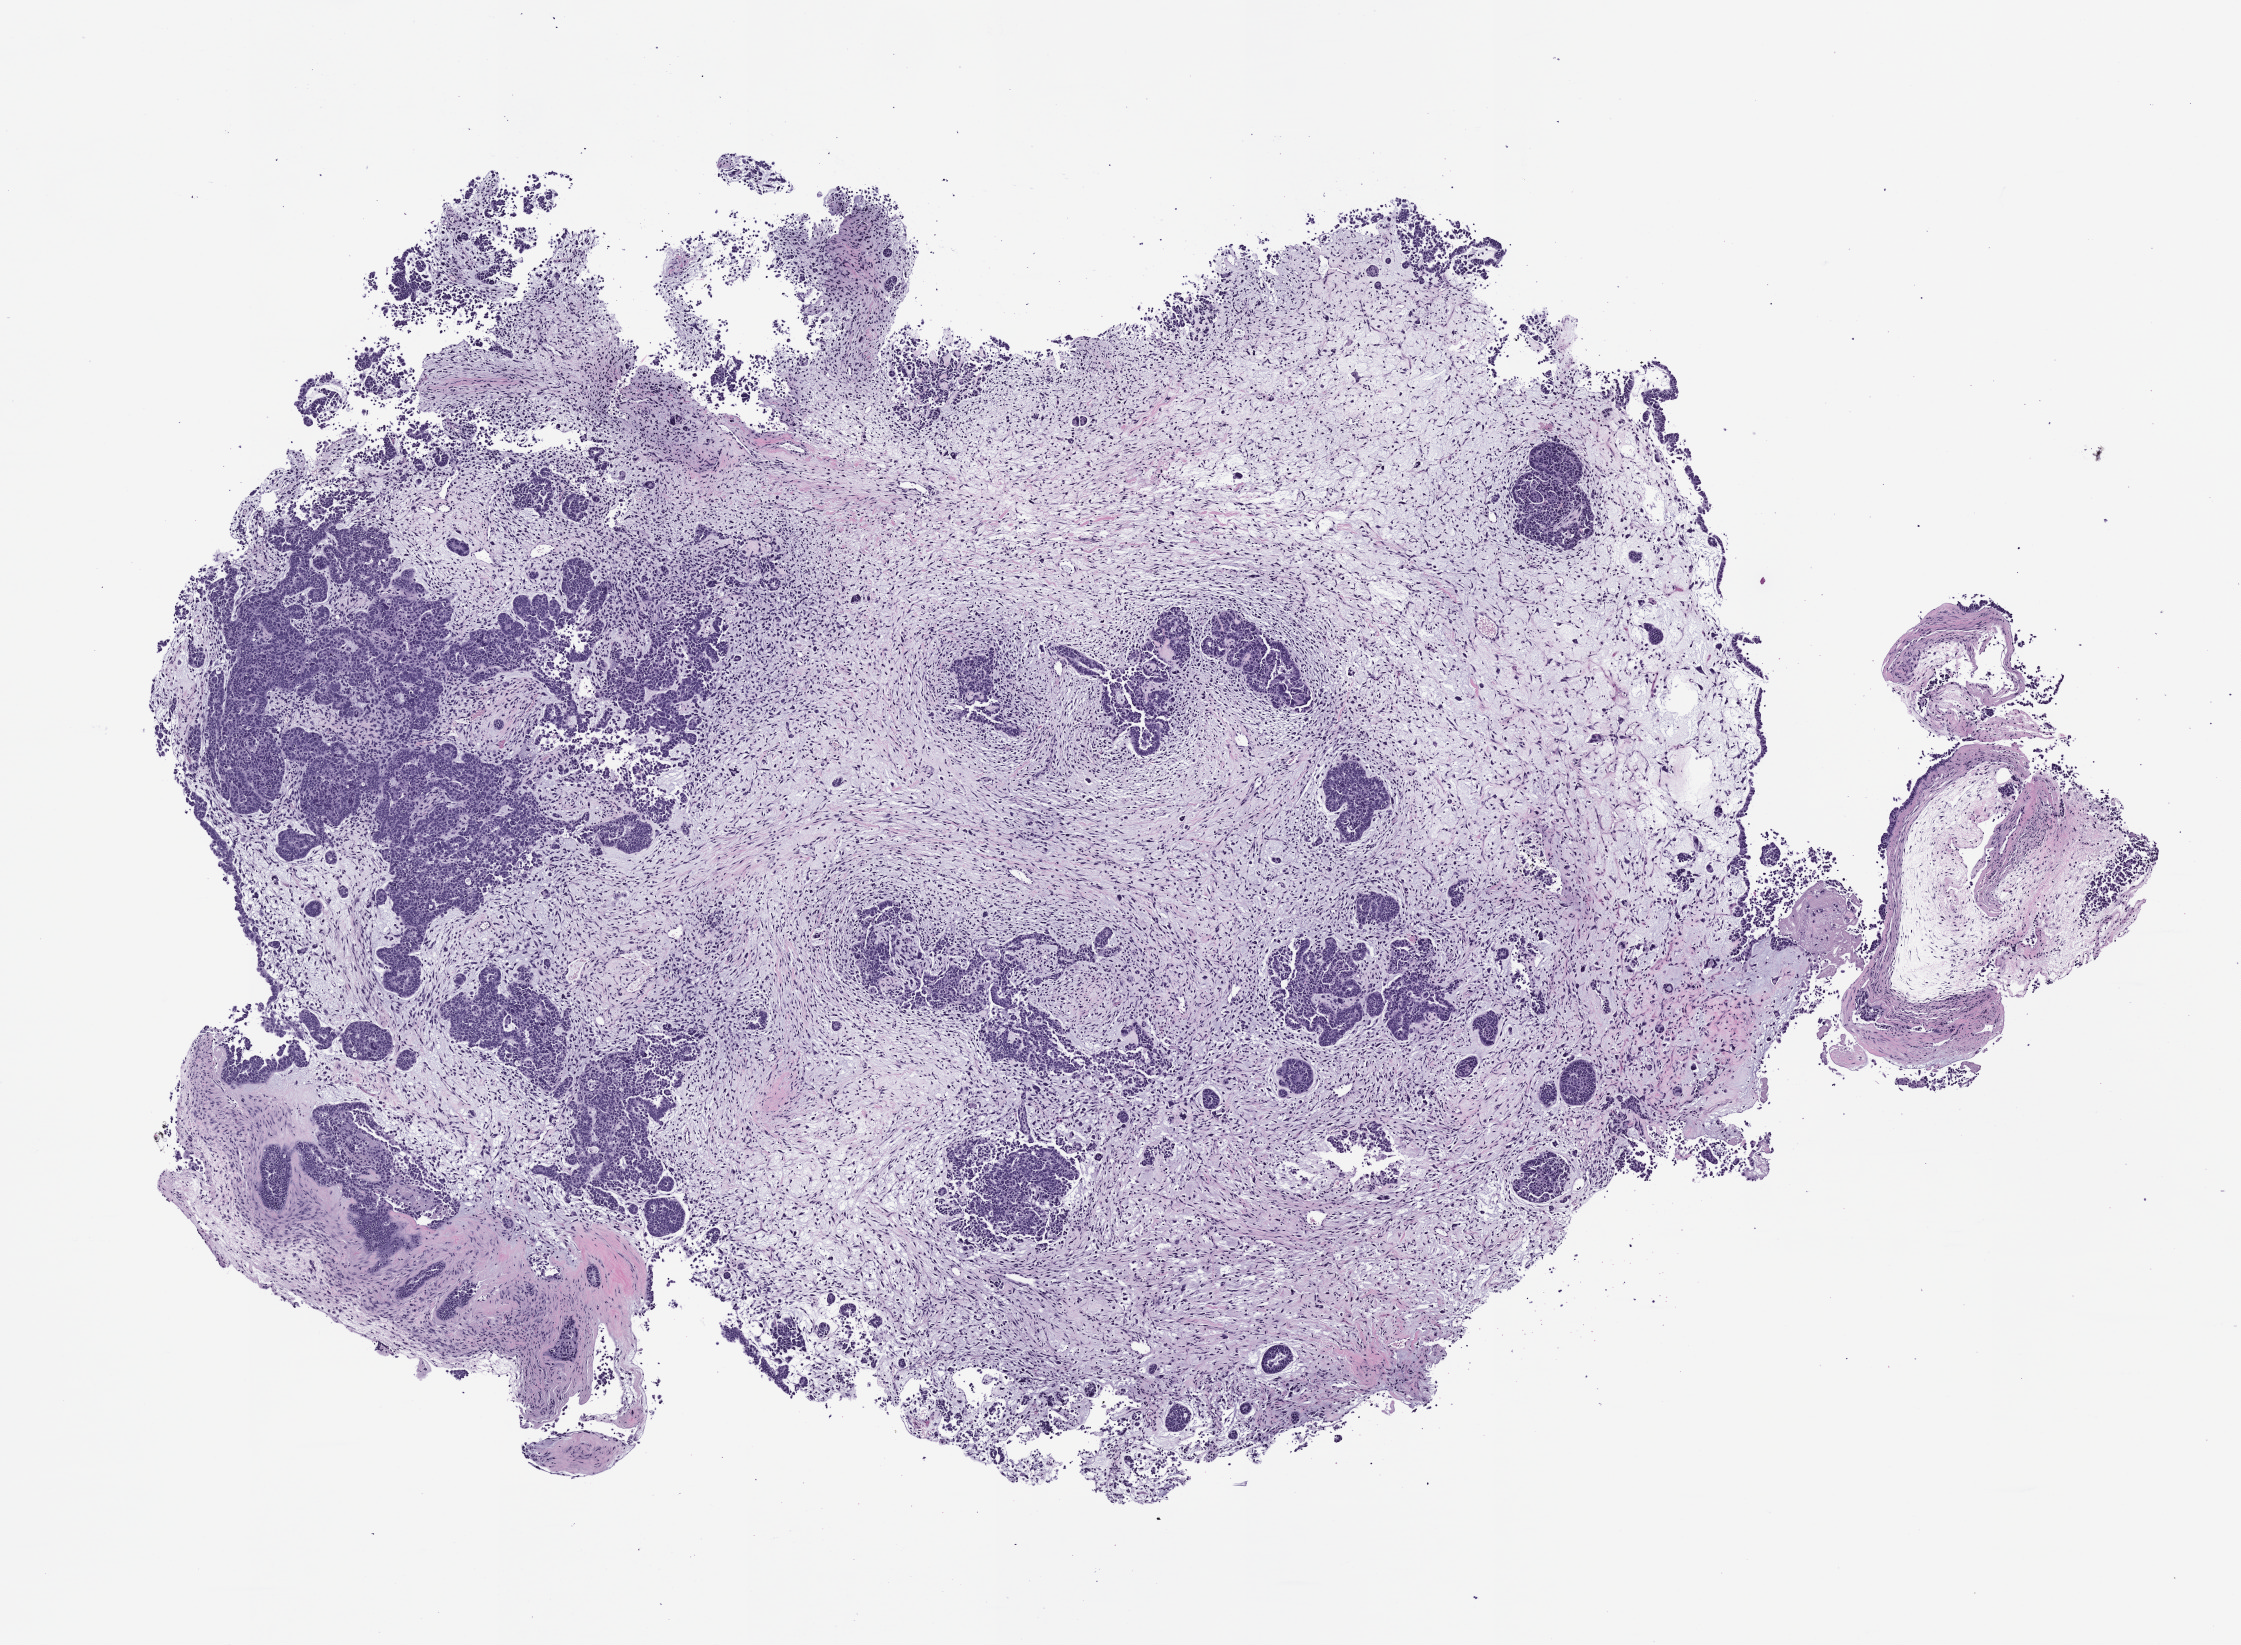
Whole-slide image, H&E: patient-derived xenograft (human tumor grown in a mouse), passage 1 — shown as a low-resolution overview of the whole scanned area (about 9.0 x 6.6 mm). Formalin-fixed, paraffin-embedded (FFPE) tissue. Tumor site category: uterus.
Originating patient diagnosis: Carcinosarcoma.